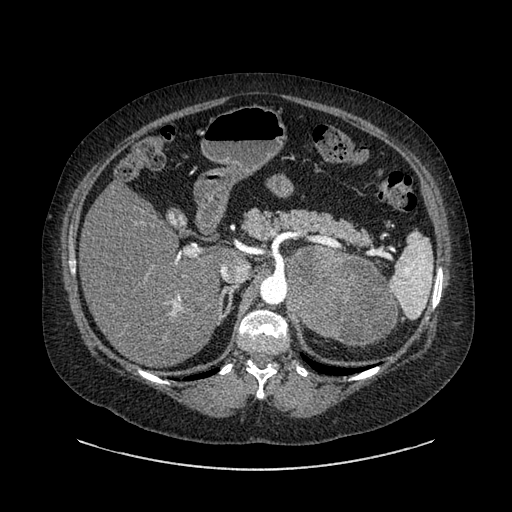
Contrast-enhanced abdominal CT, one axial slice; slice 584 of 769 in the series (ordered by position); soft-tissue window (W 400 / L 40 HU); 0.62 mm slice thickness; 512 × 512 image matrix. Patient: female, 61 years. Case-level facts recorded for this patient, not image findings: diagnosis: adrenocortical carcinoma; tumour side: left adrenal; tumour size at pathology: 13 cm; Ki-67 index: 79 %; stage (as recorded): 2.
Annotated regions visible in this slice (semi-automatically segmented with operator editing):
- mass: bounding box <288,249,396,345> (left, top, right, bottom; pixels)